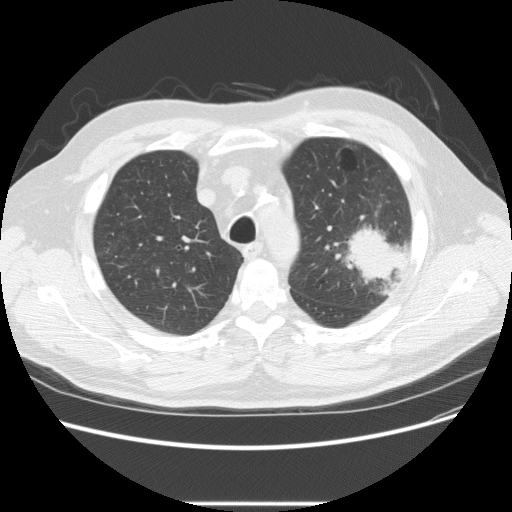
Low-dose screening chest CT, axial slice; first (baseline) screen; lung window (W 1500 / L -600 HU); 2.5 mm slice thickness. Male, age 73 years at enrolment. Former smoker at enrolment.
Lesion marked by an expert reader, bounding box (x1, y1, x2, y2) in pixels: (332, 215, 415, 285). The screening reader recorded 2 non-calcified nodules or masses ≥4 mm on this exam; which of them this box marks is not recorded. Participant outcome: lung cancer diagnosed 11 days after this screen — bronchiolo-alveolar adenocarcinoma, NOS, other location, well differentiated (G1), stage IV (AJCC 6th edition).